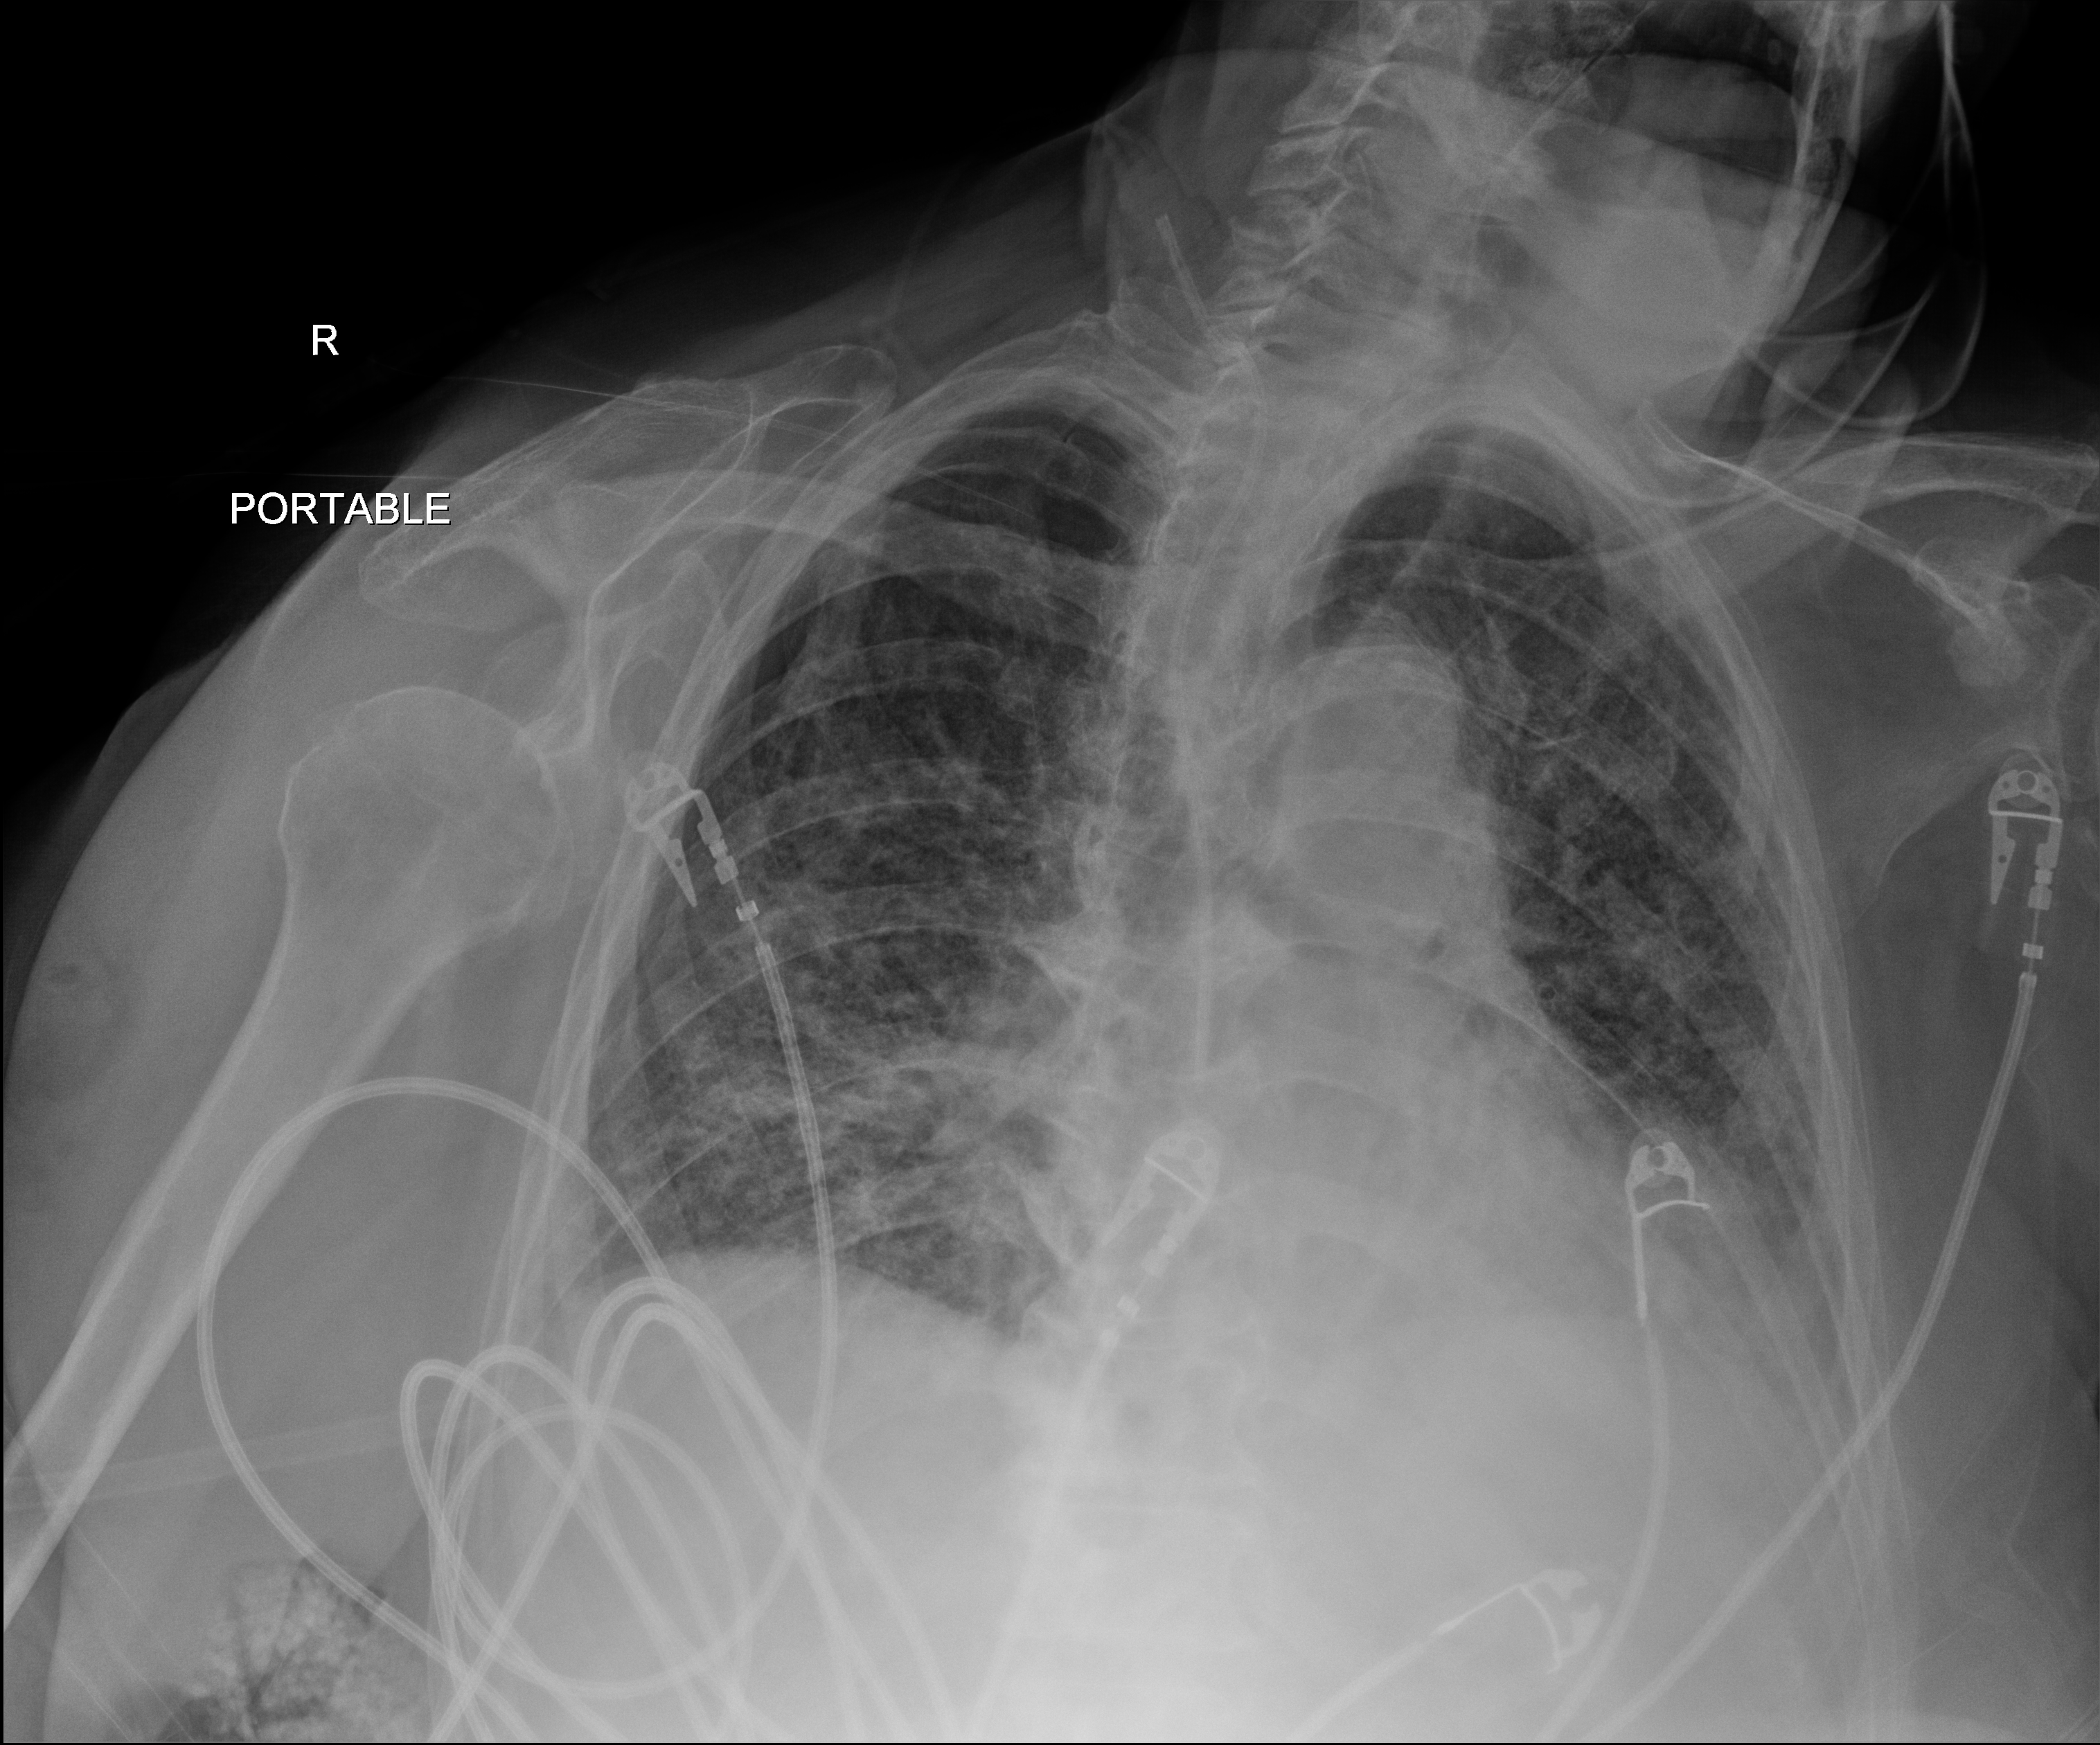
Bedside chest radiograph (digital radiography). Patient hospitalised with COVID-19; female, aged 75–90 years.
Hospital-stay facts (about this admission, not read from this image; timing relative to this image not recorded): COPD (admission record): no; admitted to intensive care during this hospital stay: no; mechanically ventilated during this hospital stay: yes.